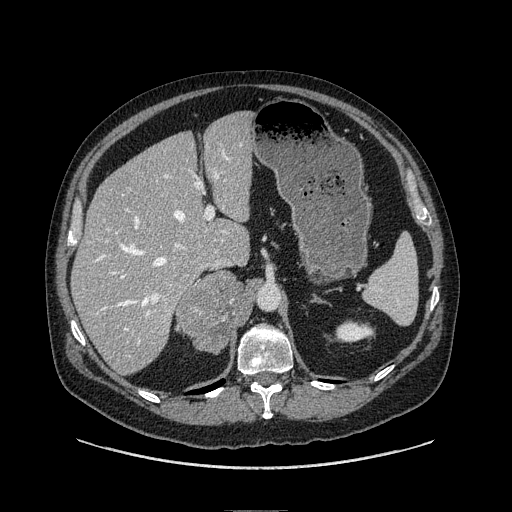
Contrast-enhanced abdominal CT, one axial slice. Position 63 of 149 along the scan axis. Soft-tissue window (W 400 / L 40 HU). 1.25 mm slice thickness. 512 × 512 image matrix, field of view 440 × 440 mm. Male patient. From the clinical record (not read from this slice): diagnosis: adrenocortical carcinoma; tumour side: right adrenal.
Structures marked on this image (semi-automatically segmented with operator editing):
- mass: bounding box [x1, y1, x2, y2] px = [178, 272, 244, 352]